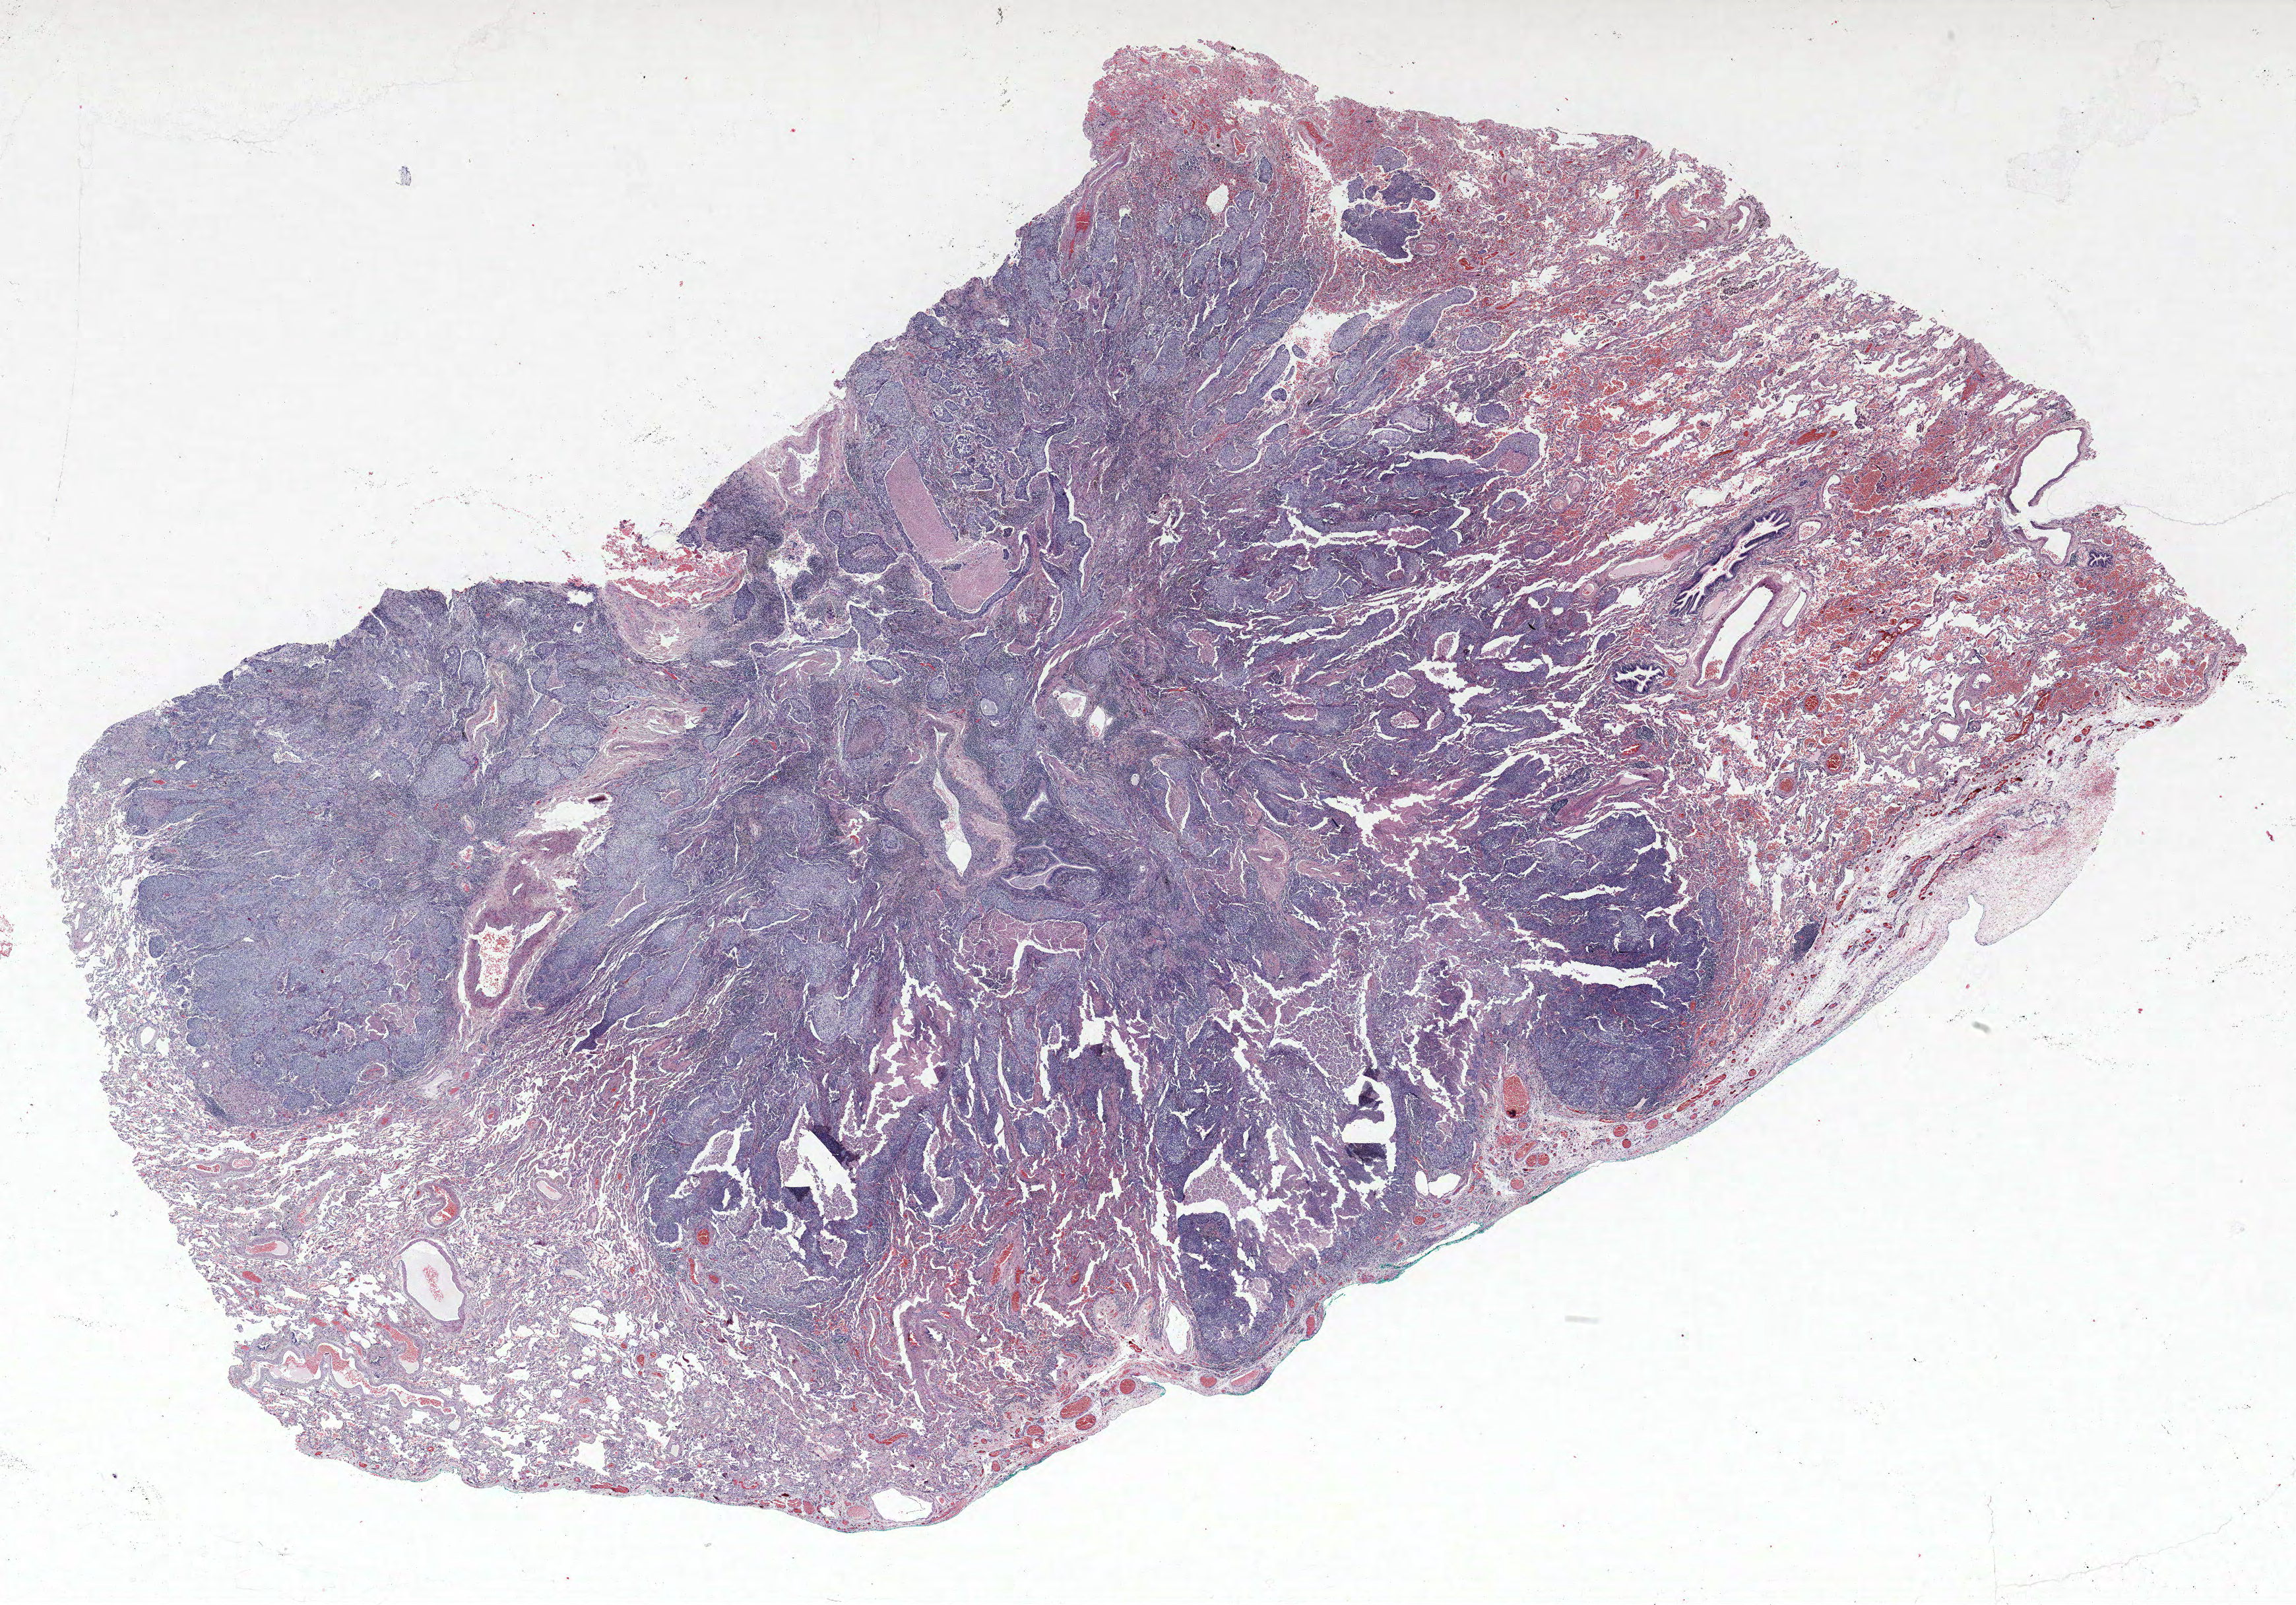
H&E-stained whole-slide image — low-resolution overview of the scanned area, about 27.8 x 19.5 mm (acquisition: 40x scan), formalin-fixed paraffin-embedded (FFPE) section, lung tissue. Male patient, aged 69 at enrolment. Current smoker at enrolment. Grade: moderately differentiated (G2).
• stage (AJCC 6th edition): IA
• tumour size (pathology): 23 mm
• primary tumour location (clinical record): right lower lobe
• participant's lung-cancer diagnosis: Squamous cell carcinoma, NOS
• ICD-O-3 topography: lower lobe of lung (C34.3)